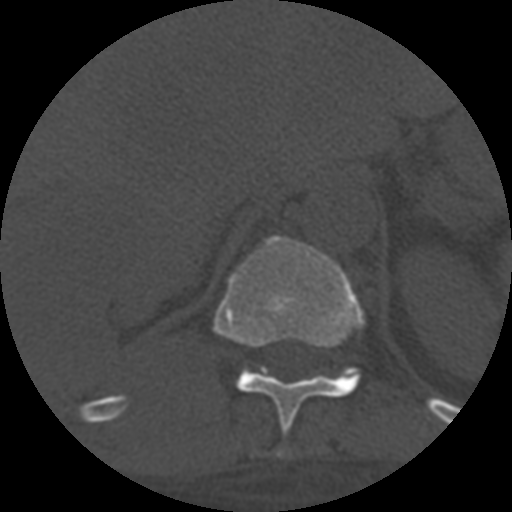
CT including the spine, one axial slice; reconstruction kernel STANDARD; 120 kVp; one of 3 acquisitions stored at this slice position; bone window (W 1800 / L 400 HU); 1.25 mm slice thickness; 512 × 512 image matrix, field of view 160 × 160 mm. Patient age 55 years. From the clinical record (not read from this slice): primary cancer: colon; vertebrae with lytic lesions (as recorded): T12, L1, L5.
Structures marked on this image (semi-automatic segmentation, software-assisted and operator-edited):
- T11 vertebra: bounding box (x1, y1, x2, y2) in pixels: (215, 236, 364, 456)
- T12 vertebra: (327, 370, 358, 379)